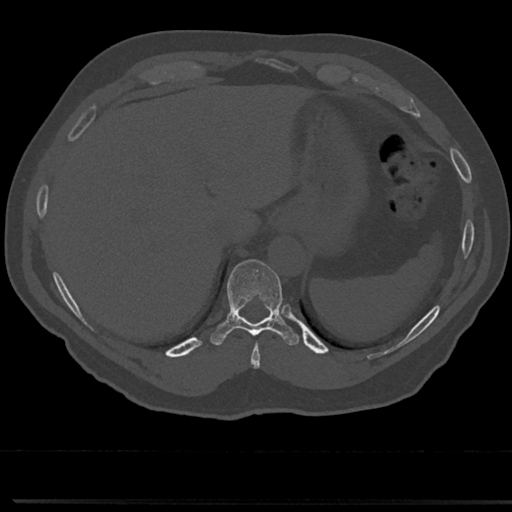
CT including the spine, one axial slice. Slice 260 of 817 in the series (ordered by position). Reconstruction kernel Br40s/3. 120 kVp. Bone window (W 1800 / L 400 HU). 0.5 mm slice thickness. 512 × 512 image matrix. Patient: male, 61 years. Case-level facts recorded for this patient, not image findings: primary cancer: prostate.
Outlined on this slice (semi-automatic segmentation, software-assisted and operator-edited):
- T10 vertebra: box from (x=213, y=260) to (x=298, y=344) px
- T9 vertebra: (x=250, y=331)–(x=264, y=358)